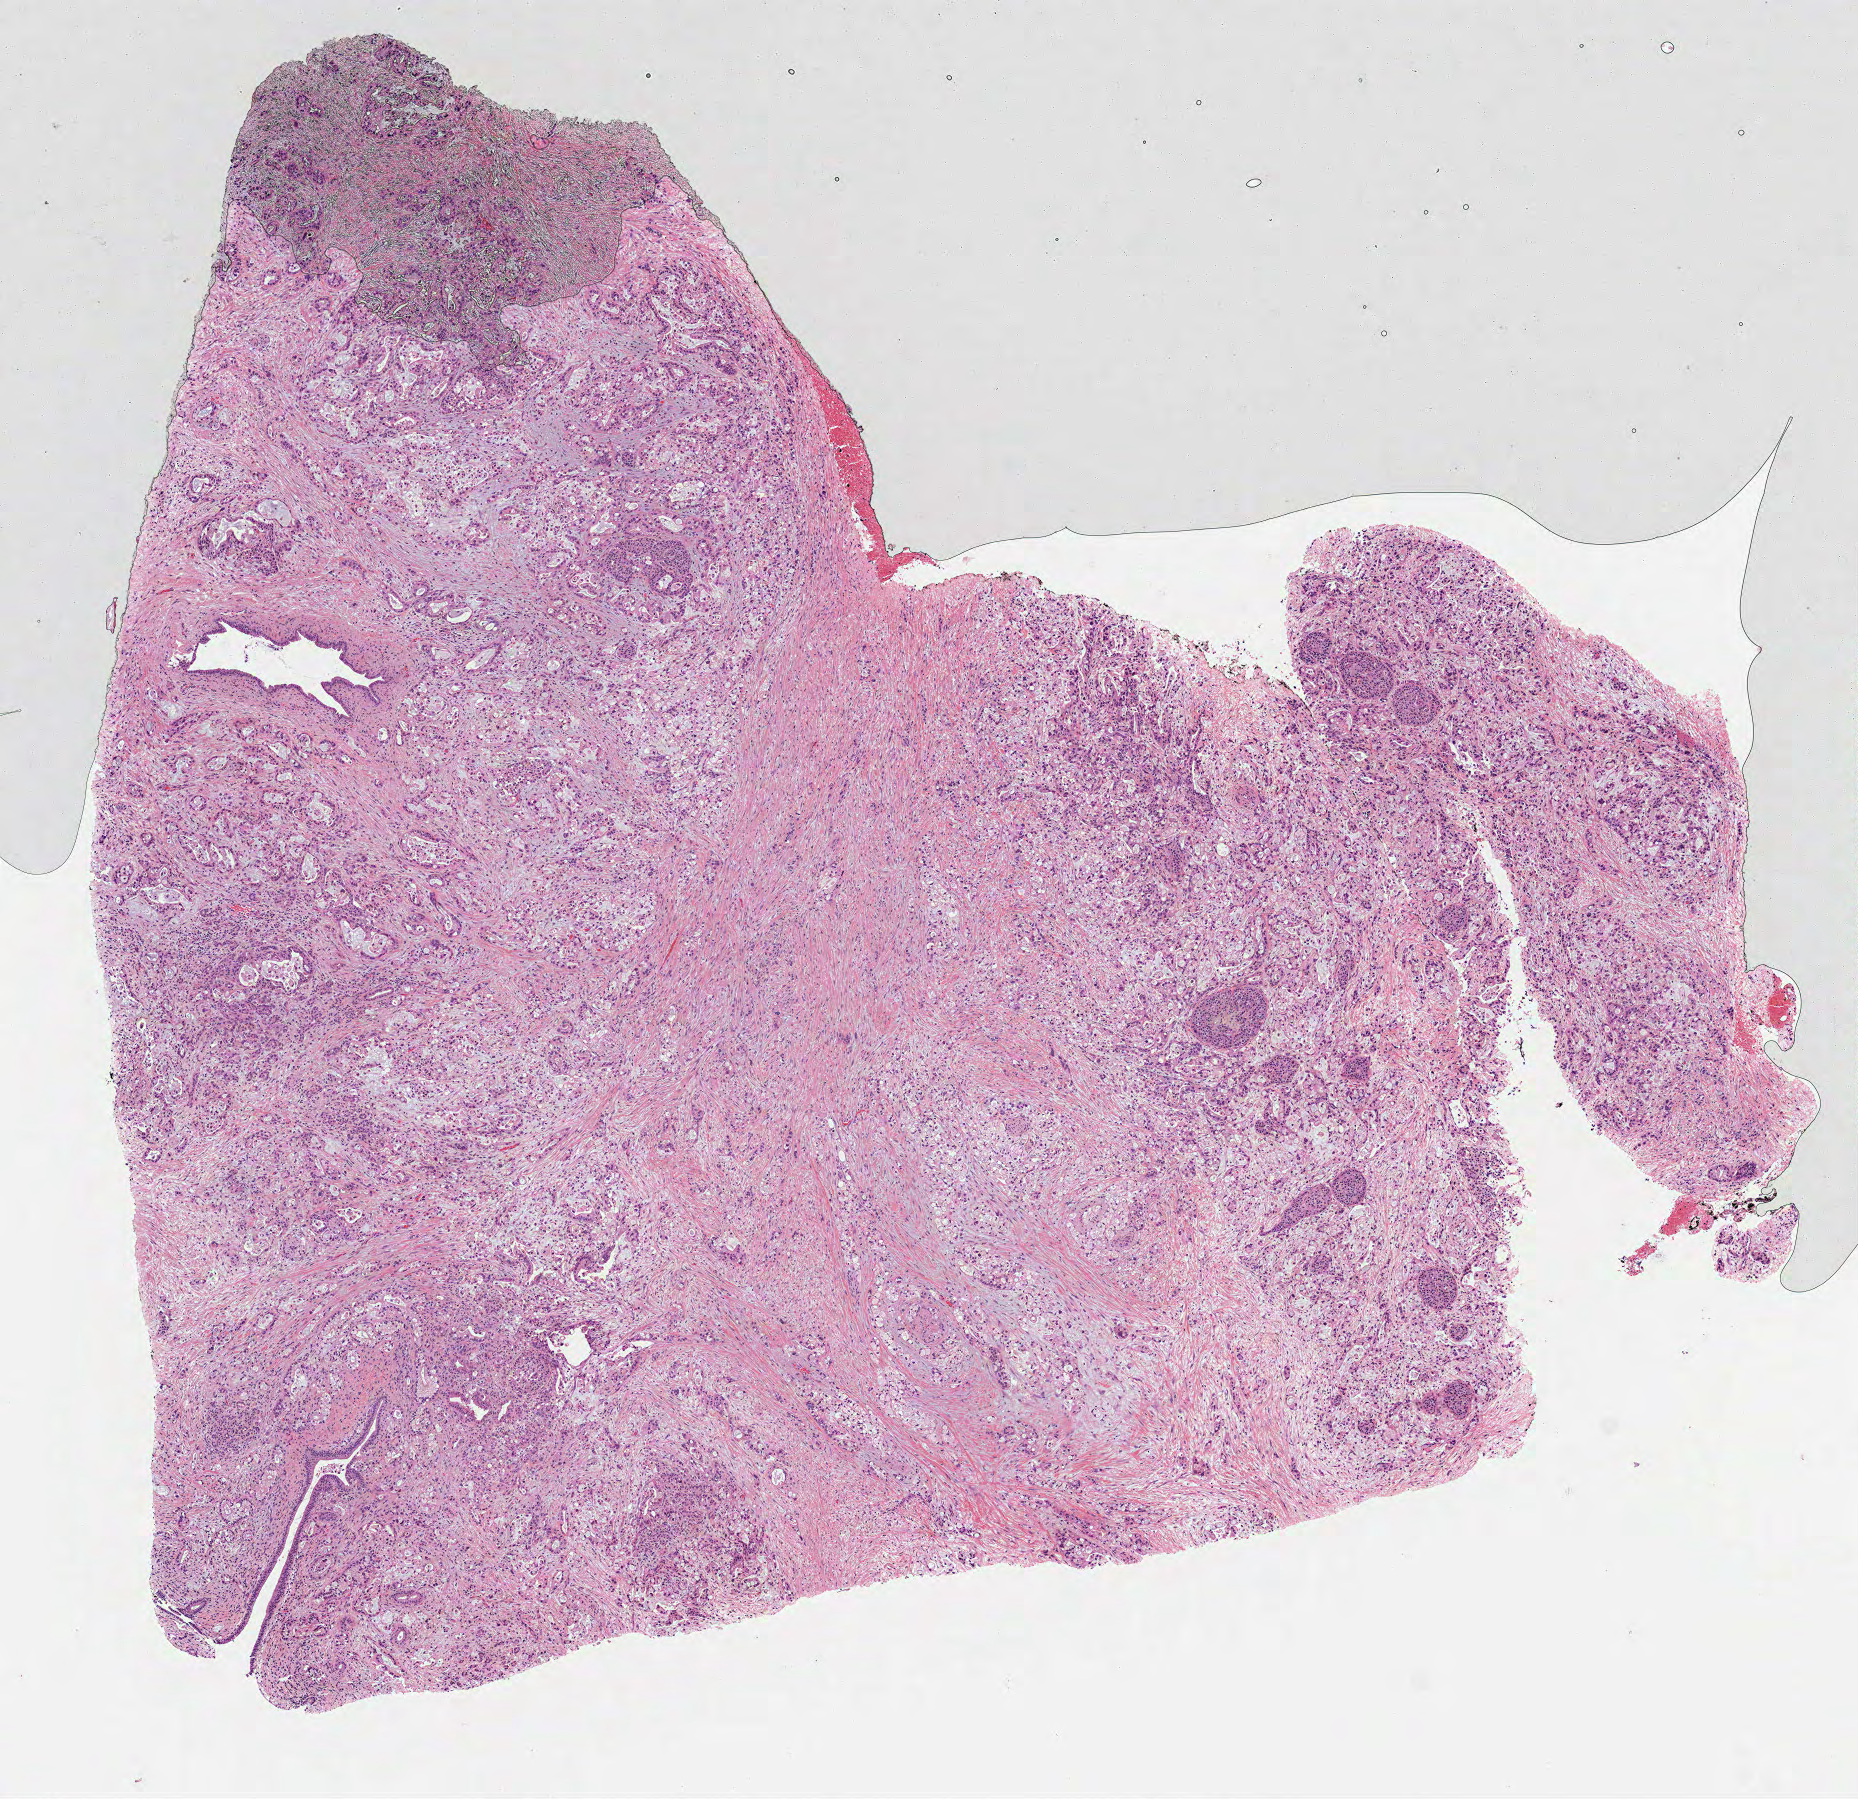
H&E-stained whole-slide image, low-resolution overview of the scanned area, about 7.5 x 7.3 mm. Formalin-fixed paraffin-embedded (FFPE) diagnostic section. Sample: primary tumour, pancreas. Patient: male, age at initial diagnosis 69 years. Histologic grade: G2 (moderately differentiated).
TNM: T4 N0 MX. AJCC pathologic stage: III (7th edition). Pathologic diagnosis: Infiltrating duct carcinoma, NOS (head of pancreas).